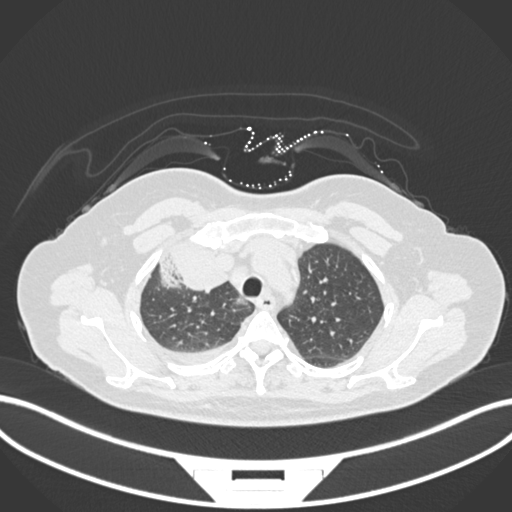
Chest CT, one axial slice. Position 129 of 172 along the scan axis. Reconstruction kernel B30f. Lung window (W 1500 / L -600 HU). 1 mm slice thickness. 512 × 512 image matrix, field of view 400 × 400 mm. Patient: female, 52 years. Case-level facts recorded for this patient, not image findings: clinical TNM (as recorded): T3 N1 M1.
Structures marked on this image (rectangle marked by the reading radiologist):
- lung tumour (recorded histology: adenocarcinoma): box from (x=158, y=243) to (x=230, y=289) px